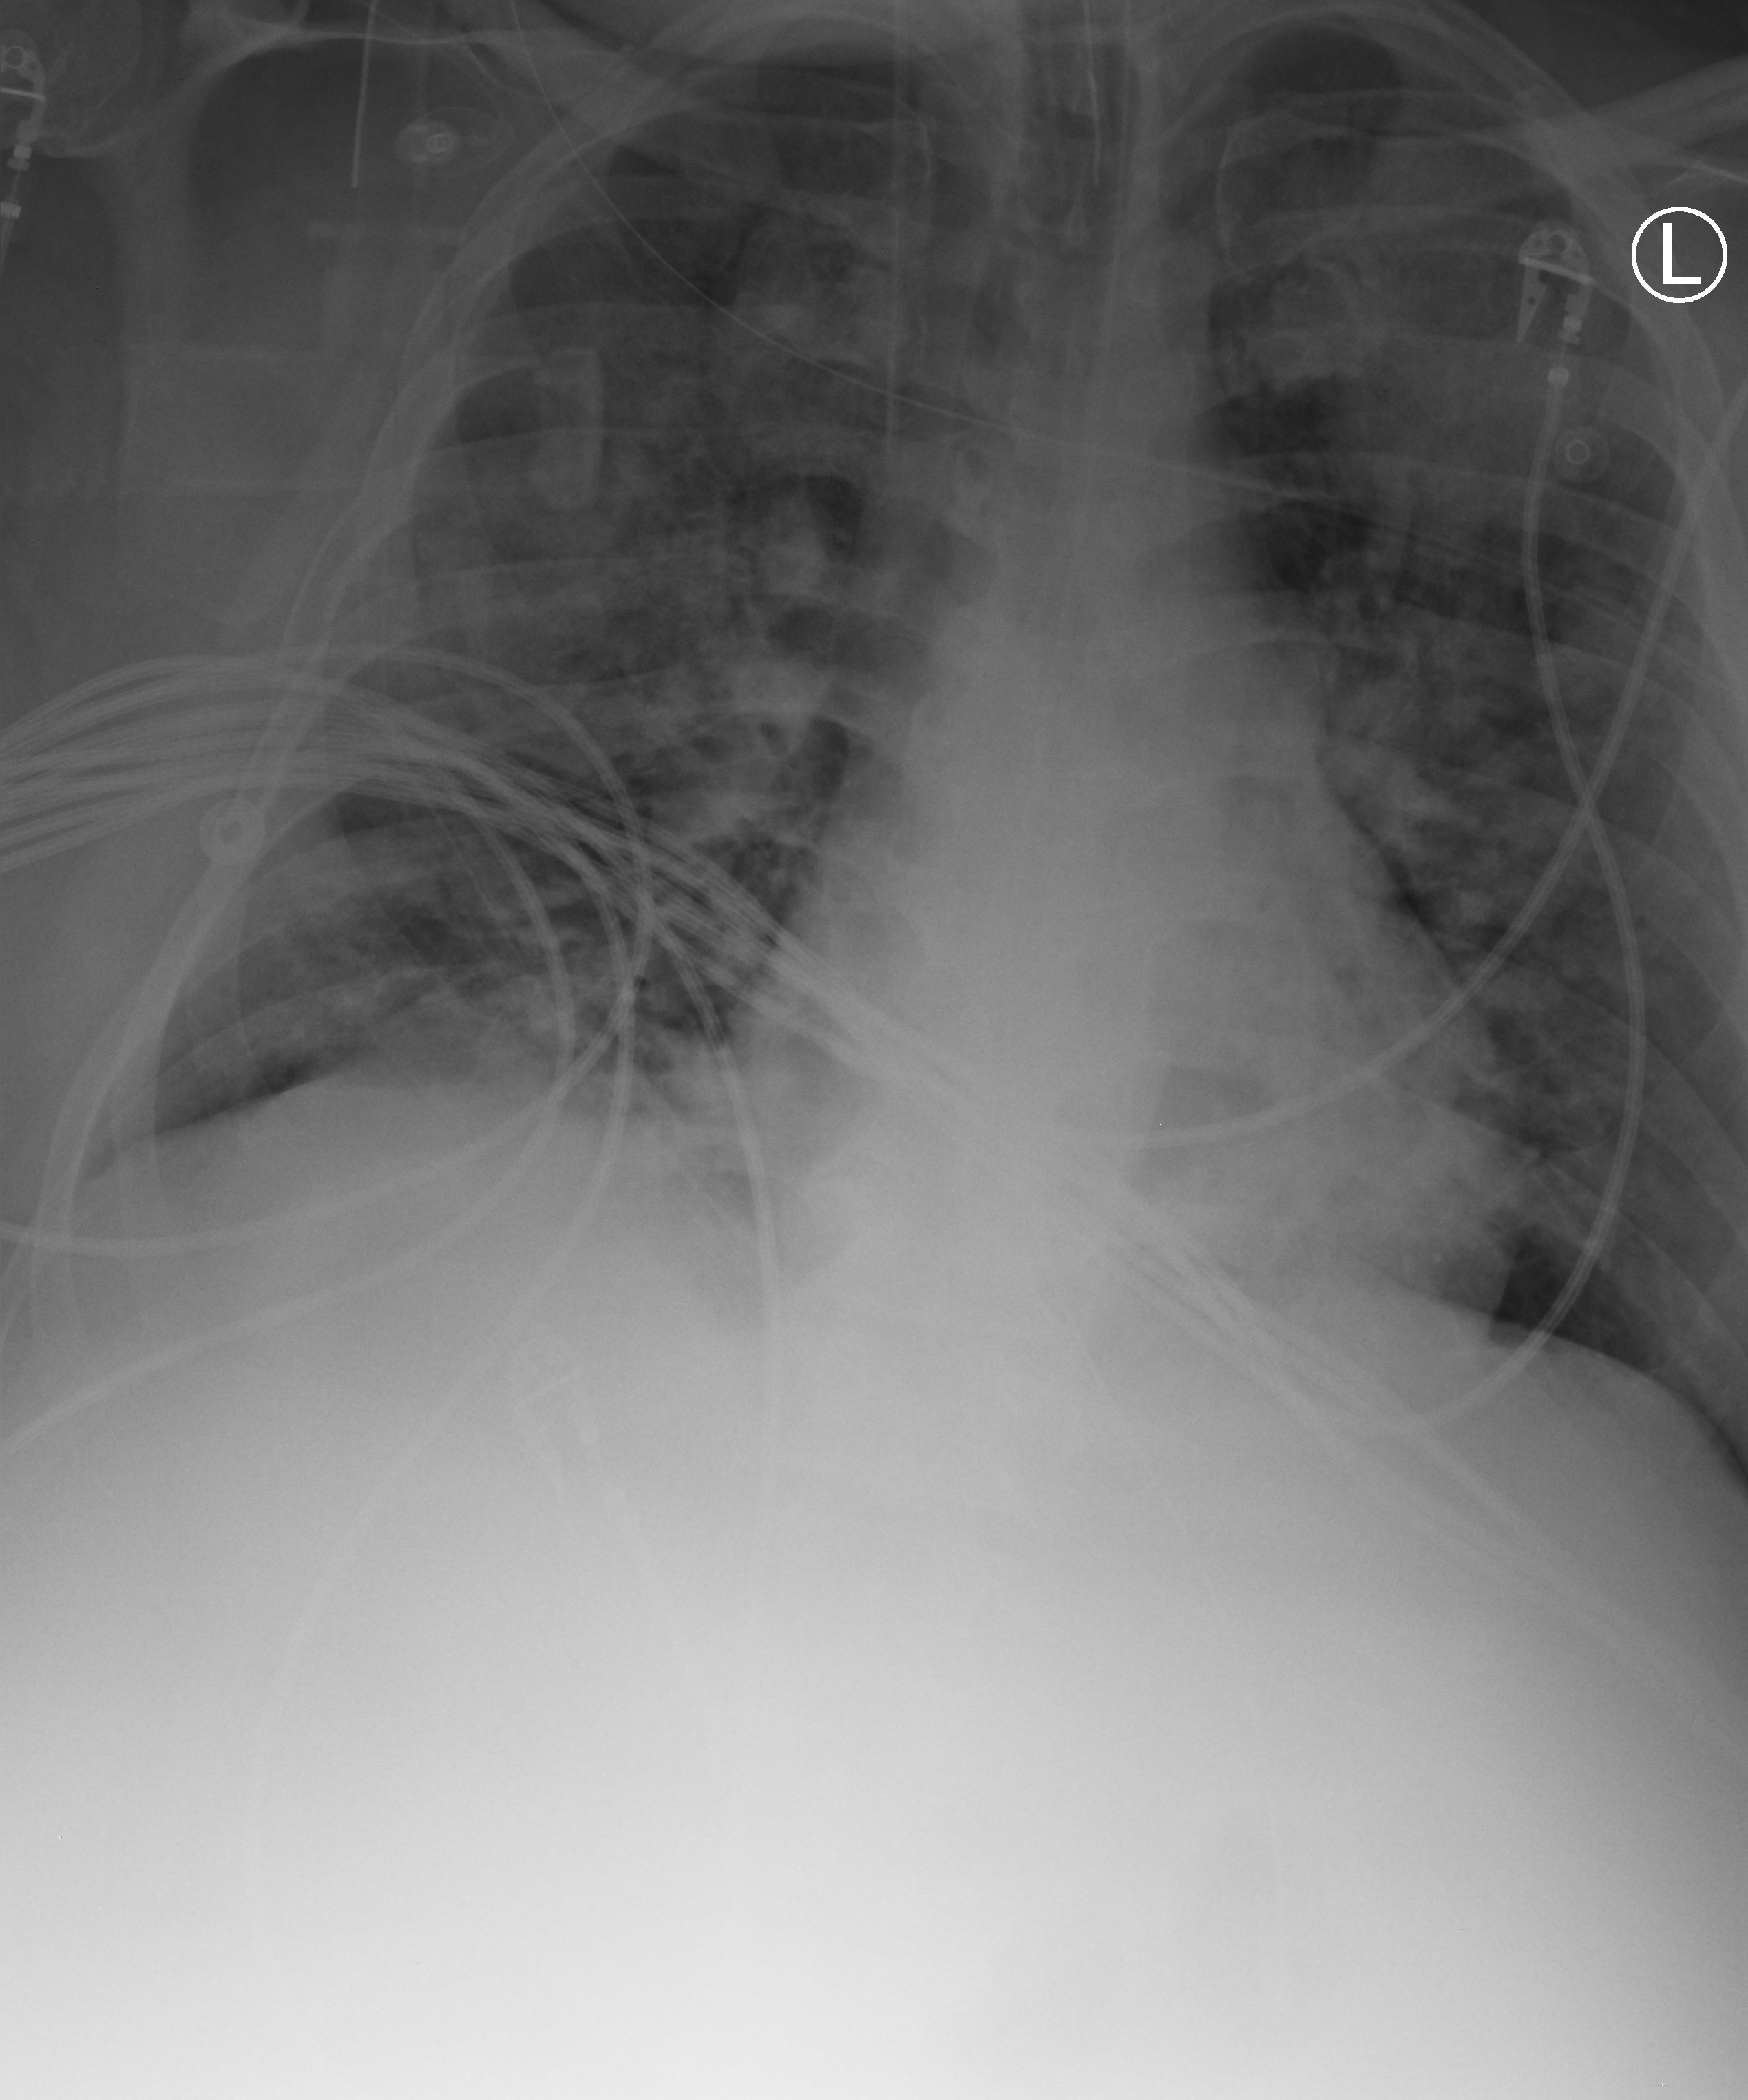
Chest X-ray (portable). Patient hospitalised with COVID-19; male, aged 18–59 years.
Admission-level facts for this patient (not findings on this image; timing relative to this image not recorded): admitted to intensive care during this hospital stay: yes; length of hospital stay: 47 days; mechanically ventilated during this hospital stay: yes.